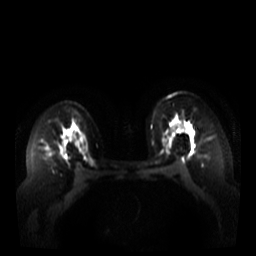
Breast MRI, one axial slice; slice 23 of 44 in the series (ordered by position); diffusion-weighted series; image 2 of 4 stored at this slice position (different b-values; order by instance number); 3 T; 5 mm slice thickness; 256 × 256 image matrix. Female patient.
Structures marked on this image (manually delineated by an expert):
- tumour on diffusion-weighted imaging: bounding box [x1, y1, x2, y2] px = [188, 130, 193, 137]